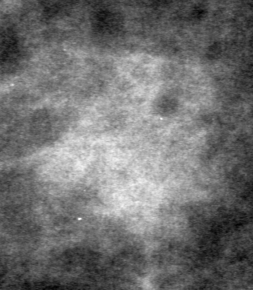
Crop from a digitized film mammogram around one marked abnormality; left breast; MLO view.
Finding: mass, shape irregular, margins ill defined; BI-RADS assessment category 4; pathology result (as recorded, not read from the image): benign.